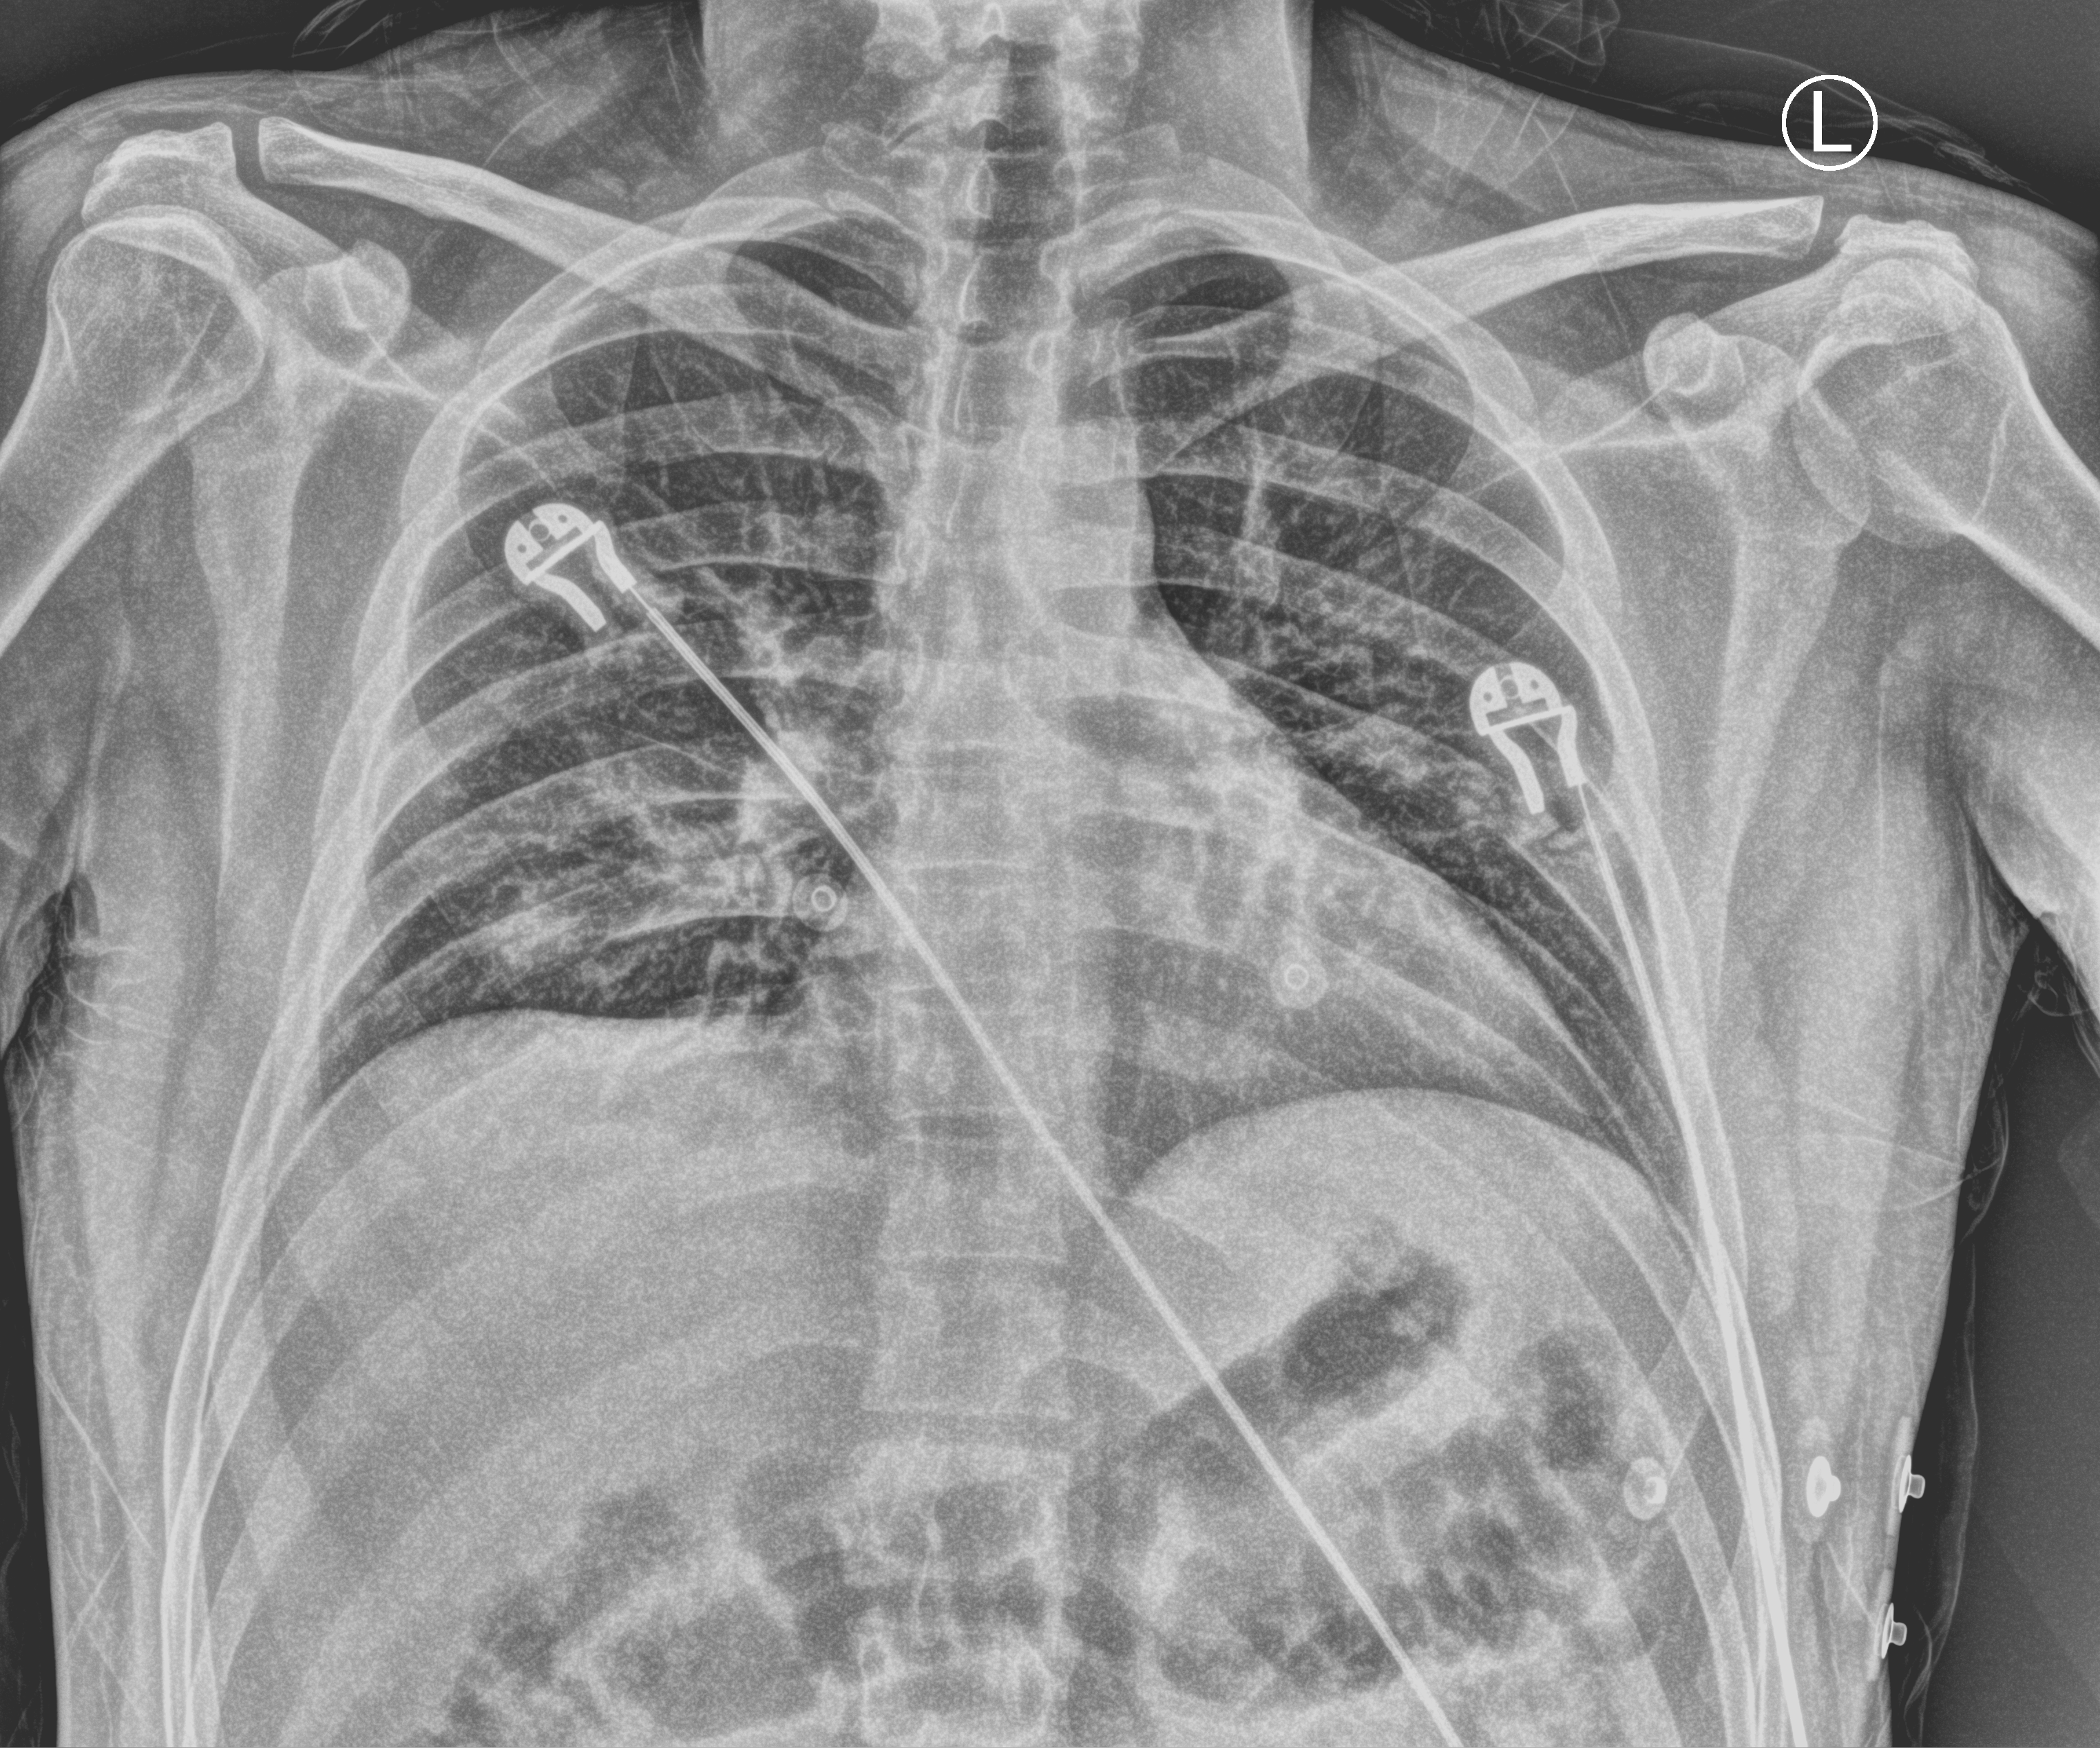
Portable chest radiograph, anteroposterior (AP) projection. Male patient hospitalised with COVID-19, age 18–59 years.
From the hospital-stay record, not from the radiograph (when in the stay this image was taken is not recorded): diabetes (admission record): no; admitted to intensive care during this hospital stay: no; mechanically ventilated during this hospital stay: no.